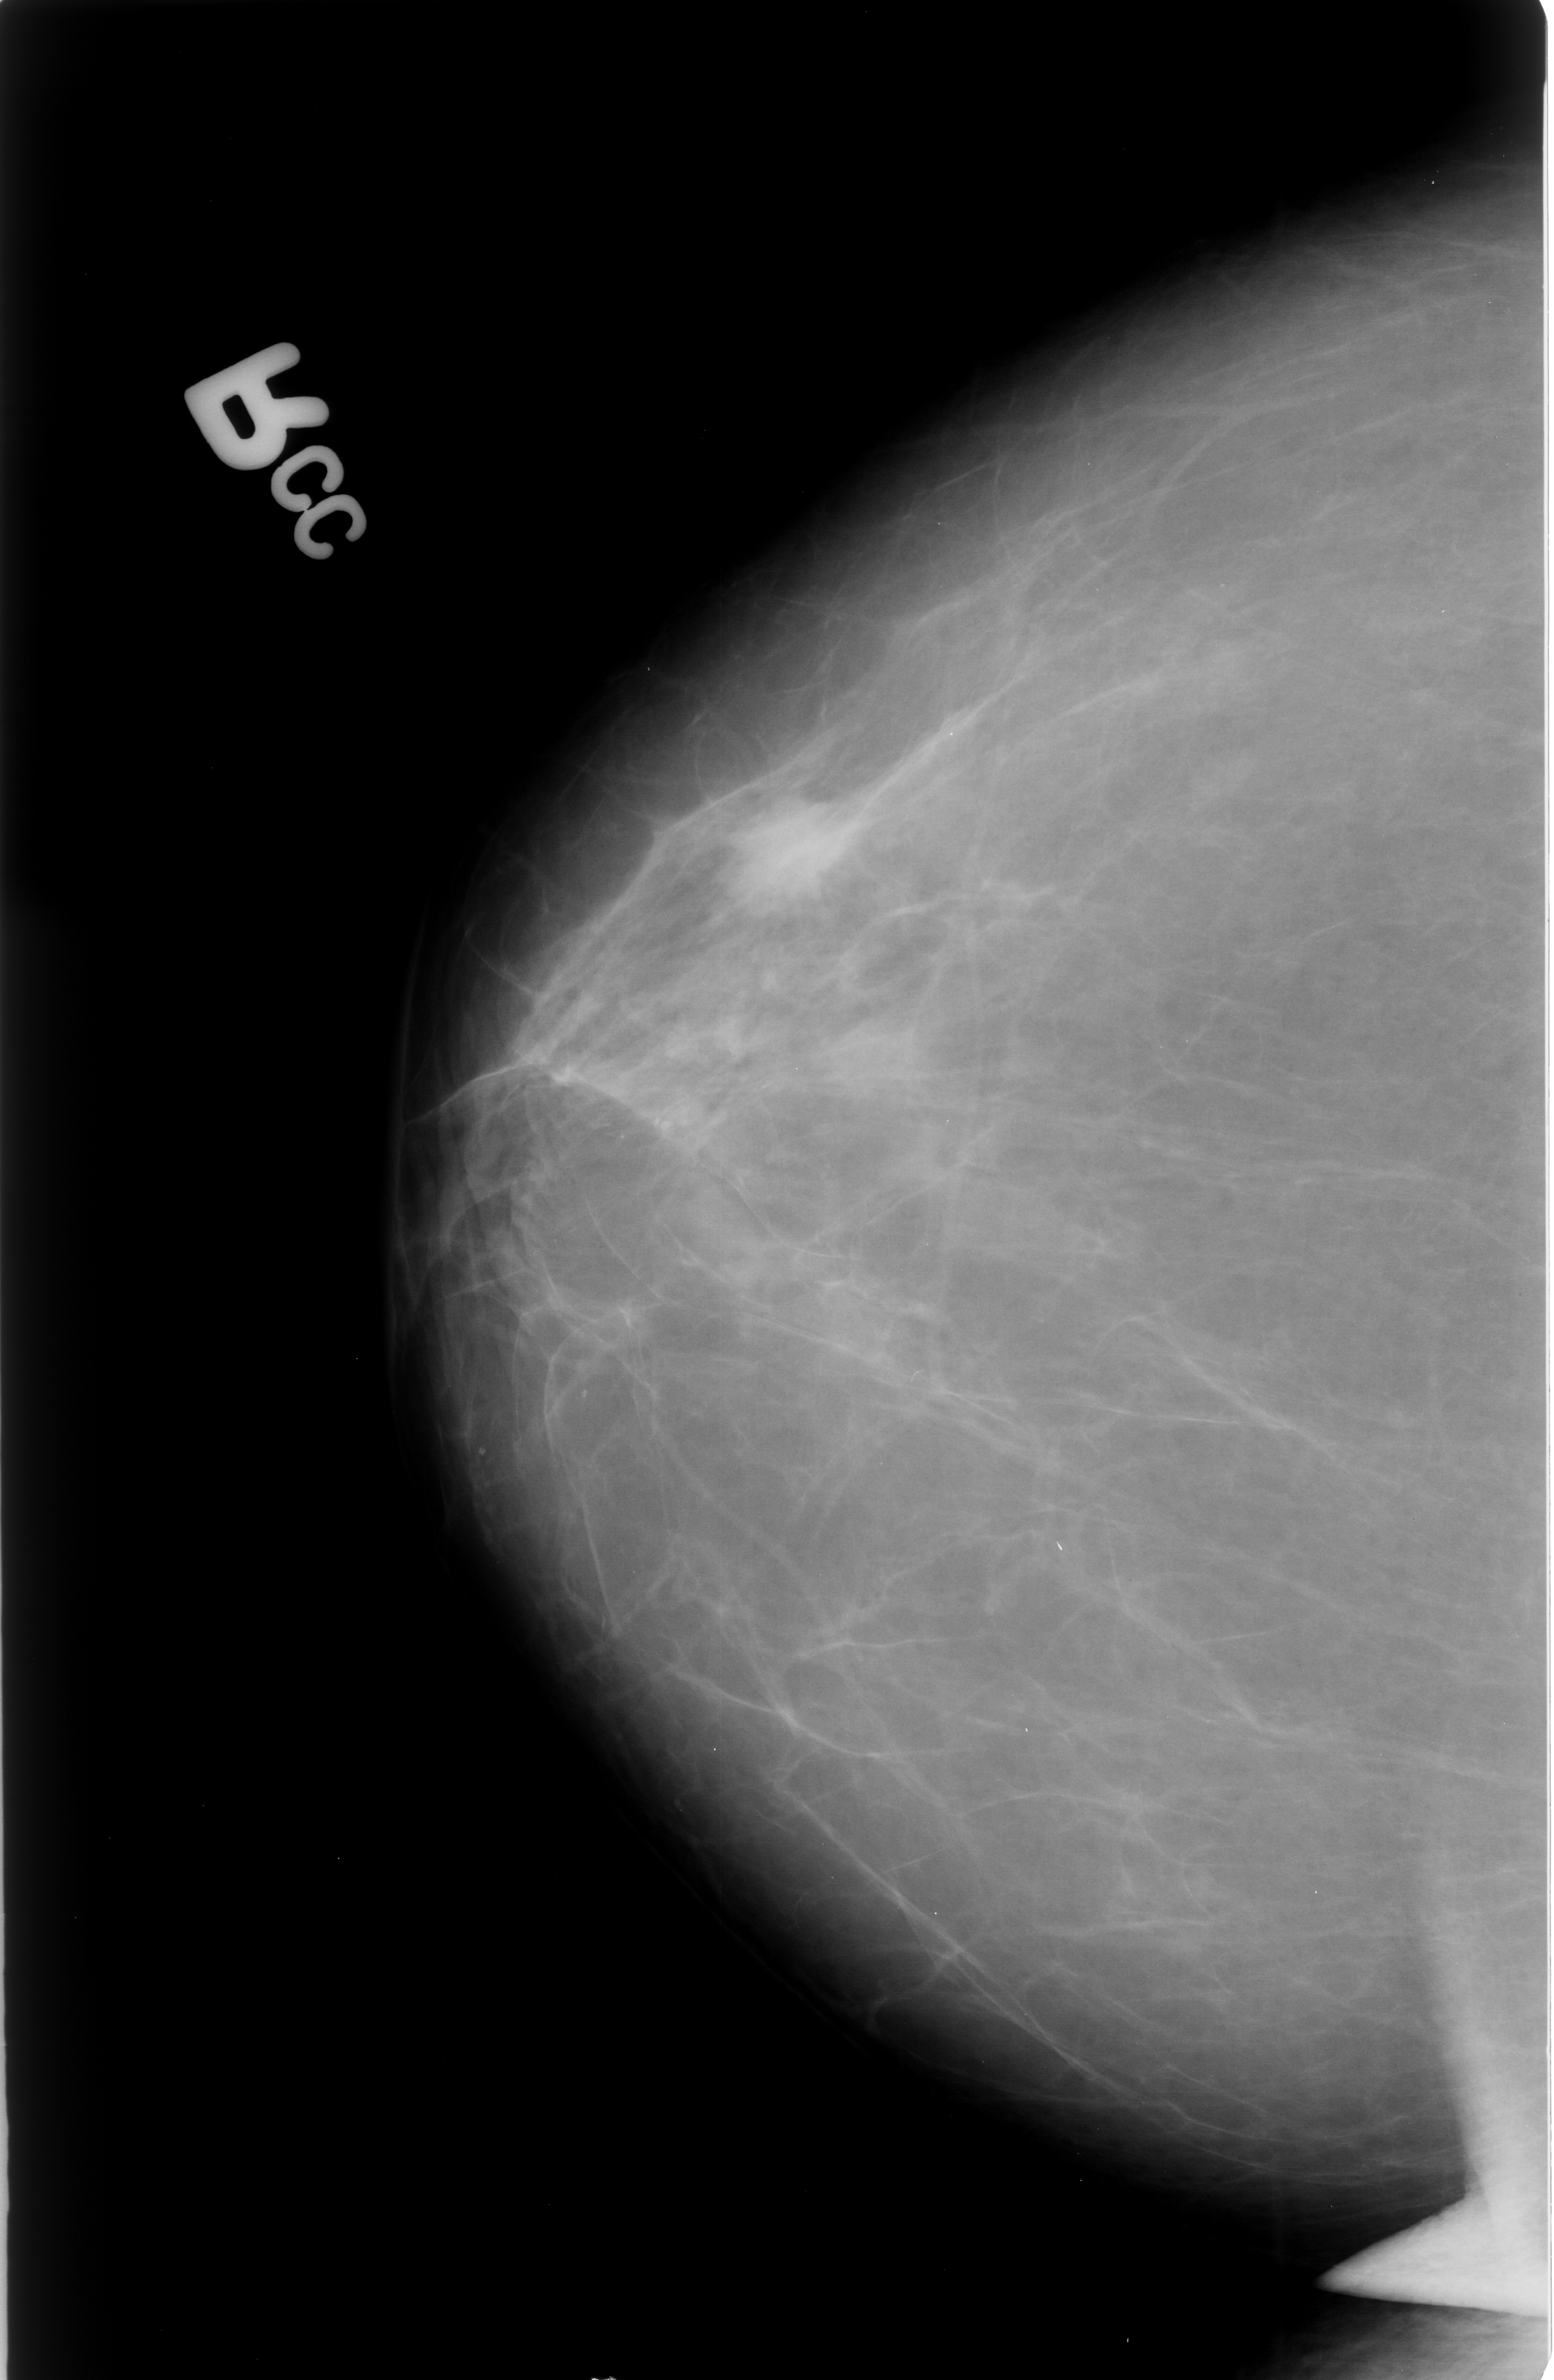
Scanned film-screen mammogram; right breast; CC view; BI-RADS breast density category 2 (scale 1–4).
- Marked findings (only marked abnormalities are described; nothing is implied about the rest of the image): mass, shape irregular, margins ill defined / spiculated; BI-RADS assessment category 4; pathology (as recorded): malignant.